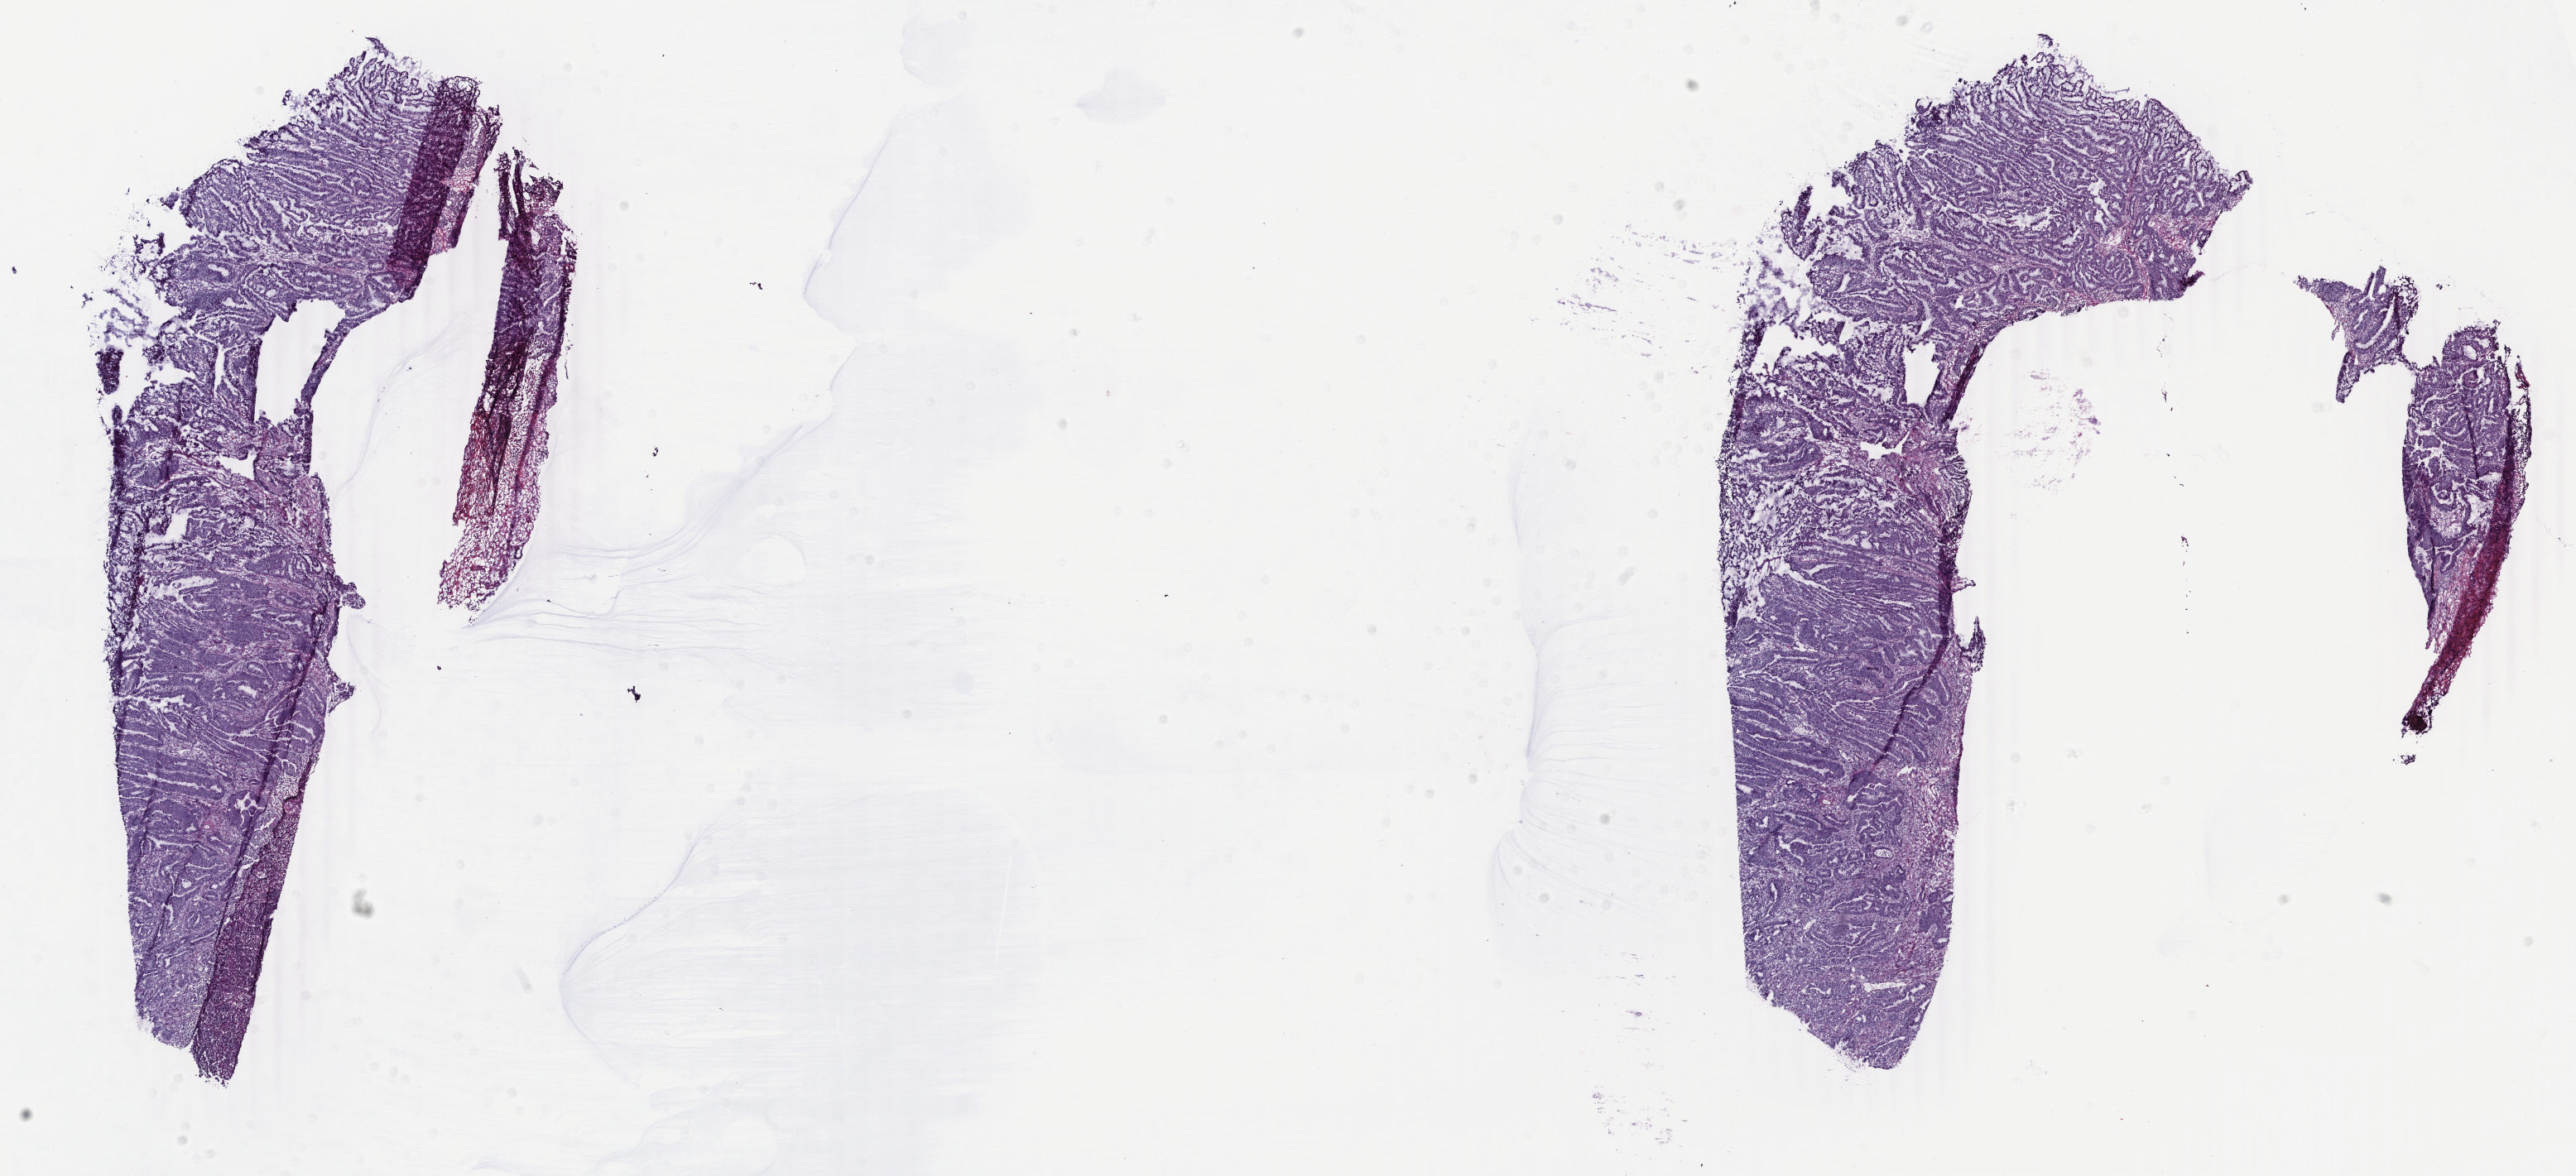
Hematoxylin and eosin (H&E) stained whole-slide image — low-resolution overview of the scanned area, about 24.7 x 11.3 mm, frozen section, primary tumour sample from the colon. Patient: male, age at initial diagnosis 82 years. Pathologist review of this section (percent, as recorded): tumour cells 93%, tumour nuclei 90%, normal cells 0%, stromal cells 5%, necrosis 2%. Inflammatory infiltration, as recorded: lymphocyte infiltration 2%, monocyte infiltration 2%, neutrophil infiltration 1%.
Lymph nodes positive (case pathology): 0 of 18 examined. AJCC pathologic stage: II (6th edition). TNM: T3 N0 M0. Pathologic diagnosis: Adenocarcinoma, NOS (transverse colon).